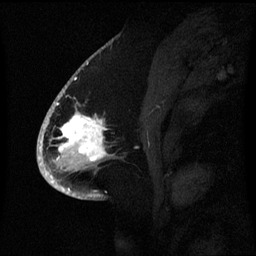
Breast MRI (dynamic contrast-enhanced), one sagittal slice; position 35 of 60 along the scan axis; dynamic contrast-enhanced series, image 2 of 3 at this slice position (ordered by acquisition); 1.5 T; TE 4.2 ms, TR 8.4 ms; 2.1 mm slice thickness; 256 × 256 image matrix, field of view 220 × 220 mm. Female patient, age 53 years. Case-level facts recorded for this patient, not image findings: setting: breast cancer imaged before/during neoadjuvant chemotherapy; receptor status: HR-positive, HER2-negative.
Annotated regions visible in this slice (semi-automatically segmented with operator editing):
- analysis volume of interest (the breast-tissue region the enhancement analysis was run in; not a lesion): bounding box [x1, y1, x2, y2] px = [52, 90, 117, 171]
- tumour enhancement mask (voxels above the 70 % enhancement threshold inside the analysis volume of interest): [56, 90, 107, 161]